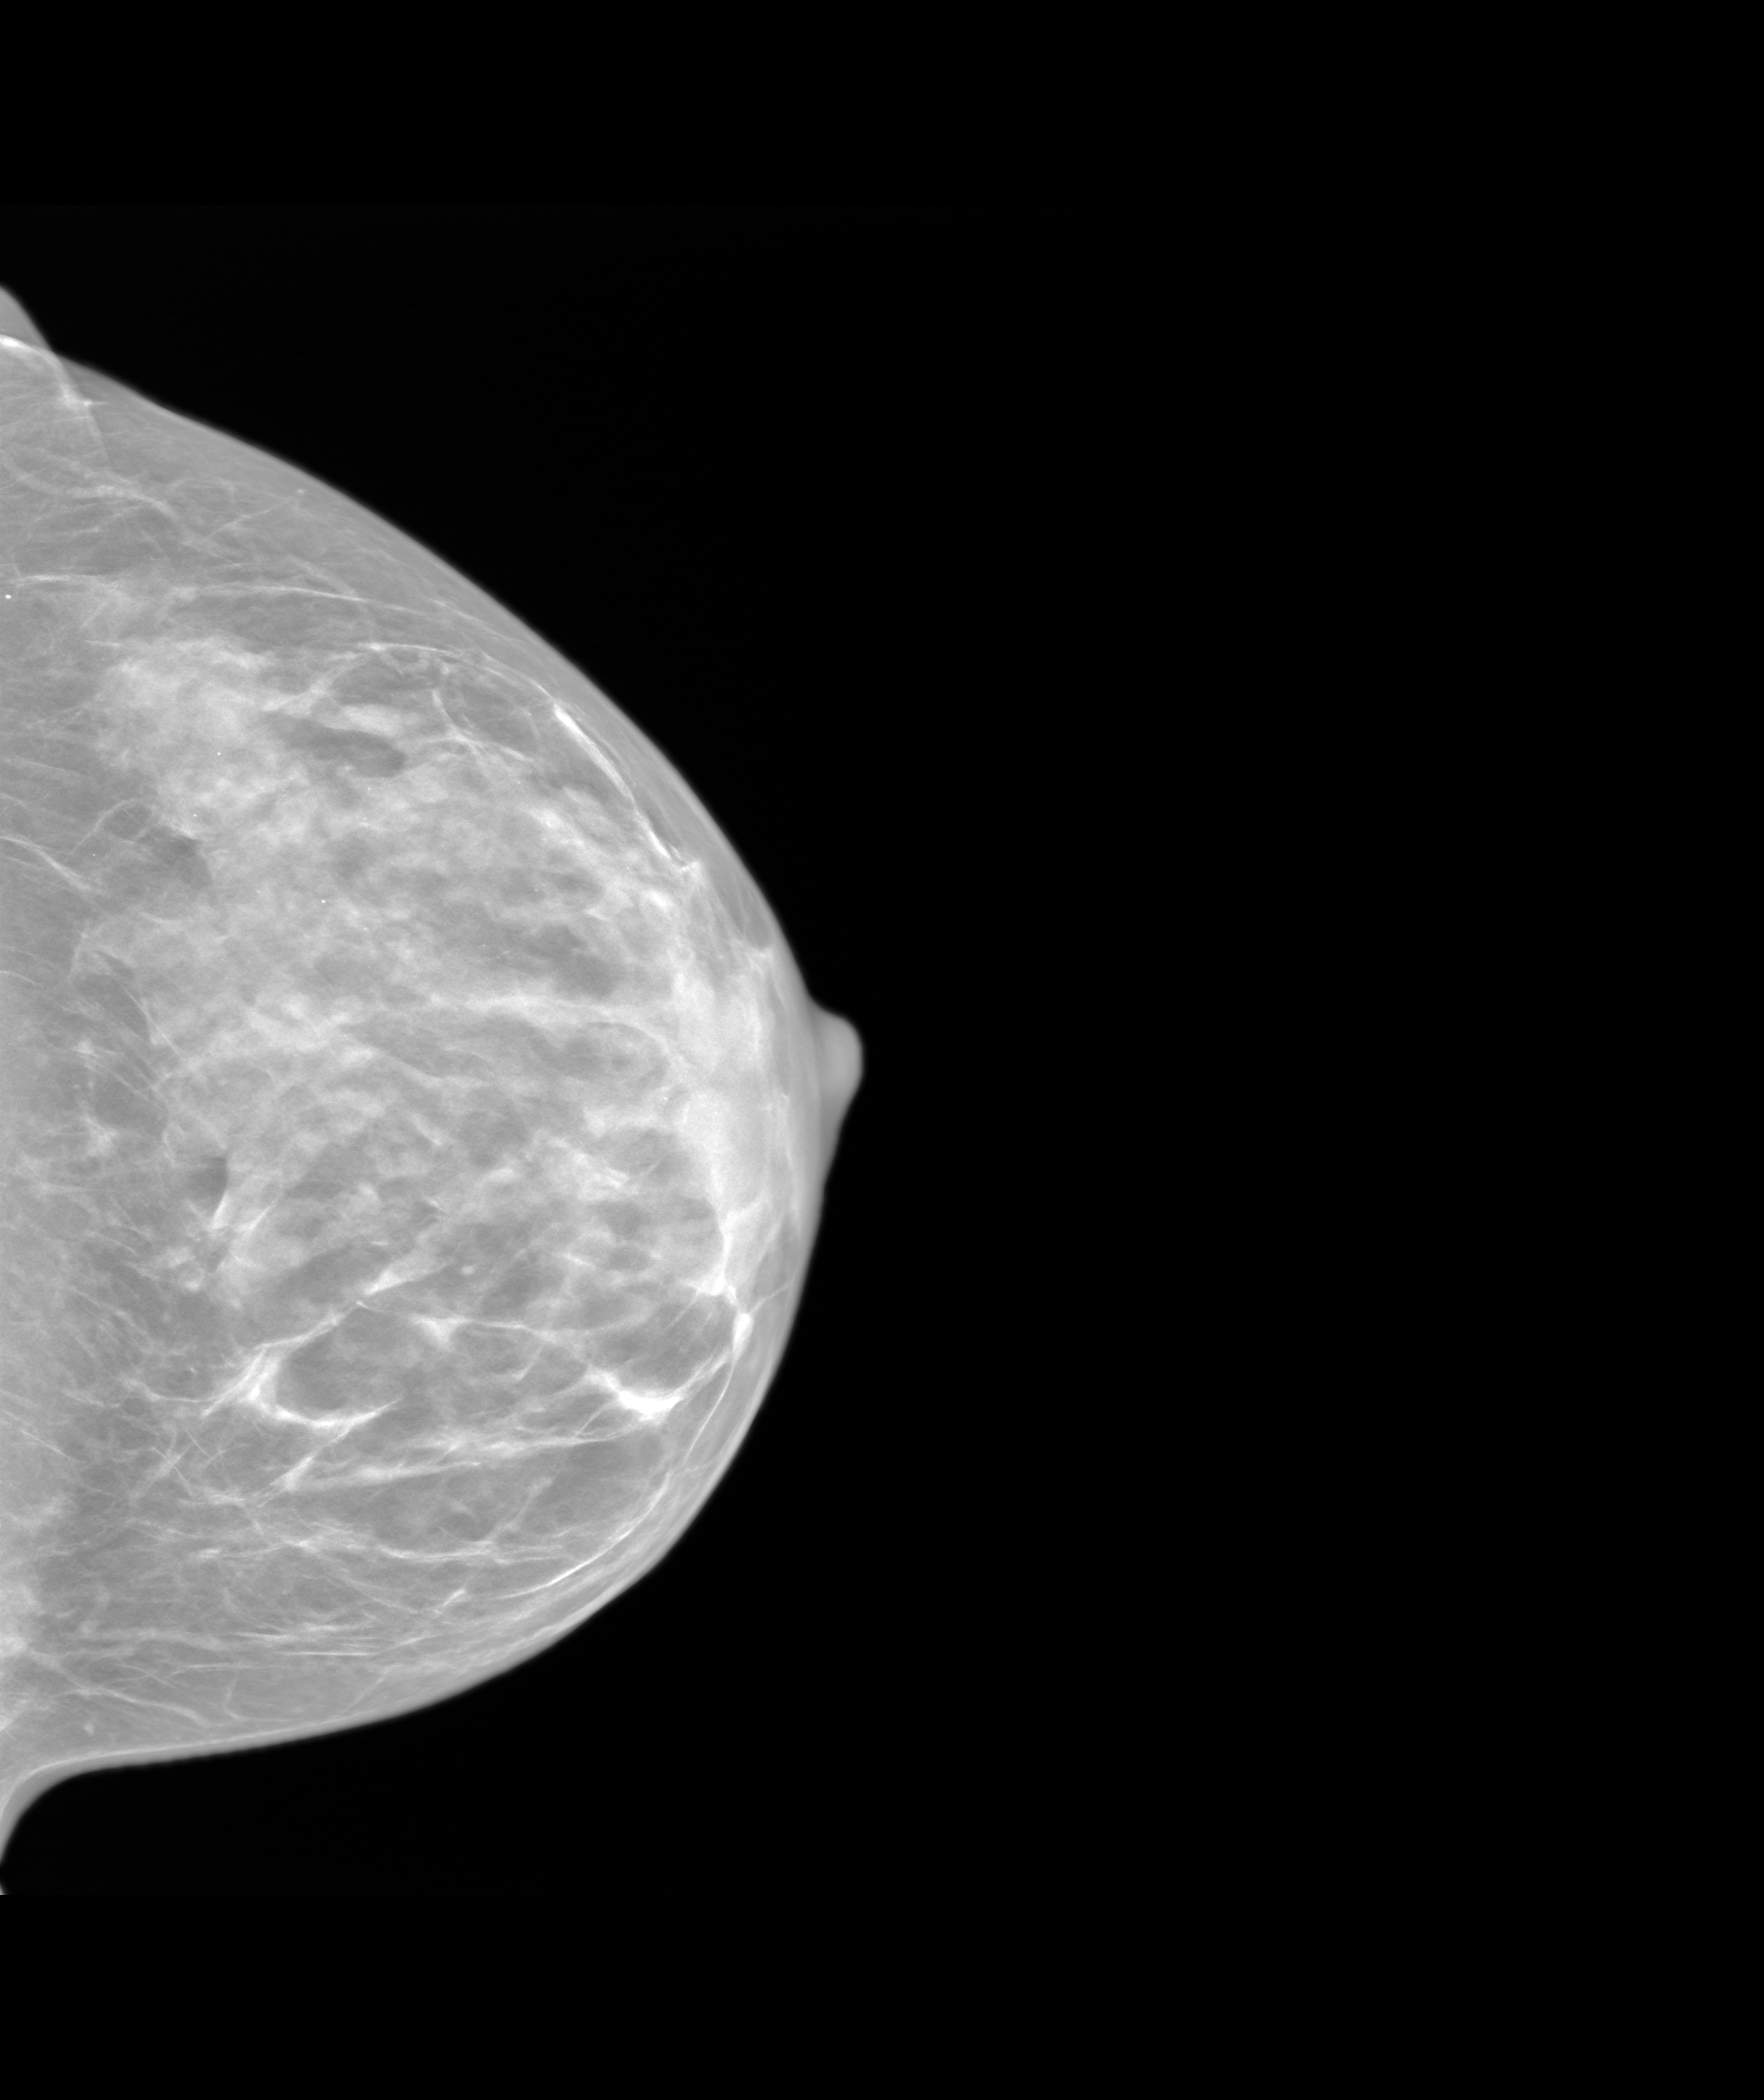
Screening examination. Patient: female, 48 years.
Image type: synthesized 2-D view from tomosynthesis. Breast: left. Projection: CC view.